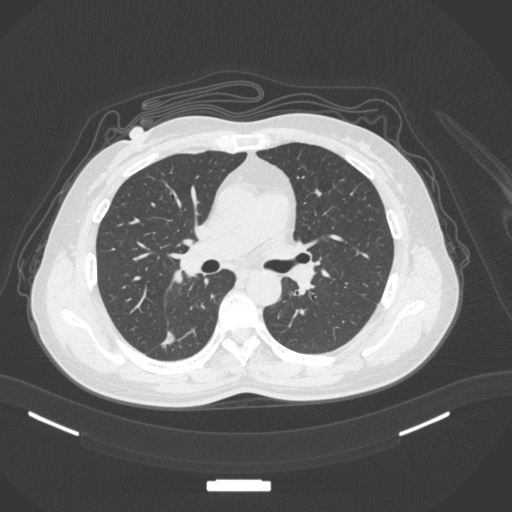
Chest CT, one axial slice. Position 178 of 352 along the scan axis. Lung window (W 1500 / L -600 HU). 1 mm slice thickness. 512 × 512 image matrix, field of view 400 × 400 mm. Female patient, age 55 years. Case-level facts recorded for this patient, not image findings: clinical TNM (as recorded): T1c N1 M0.
Annotated regions visible in this slice (rectangle marked by the reading radiologist):
- lung tumour (recorded histology: adenocarcinoma): bounding box [x1, y1, x2, y2] px = [155, 330, 182, 353]